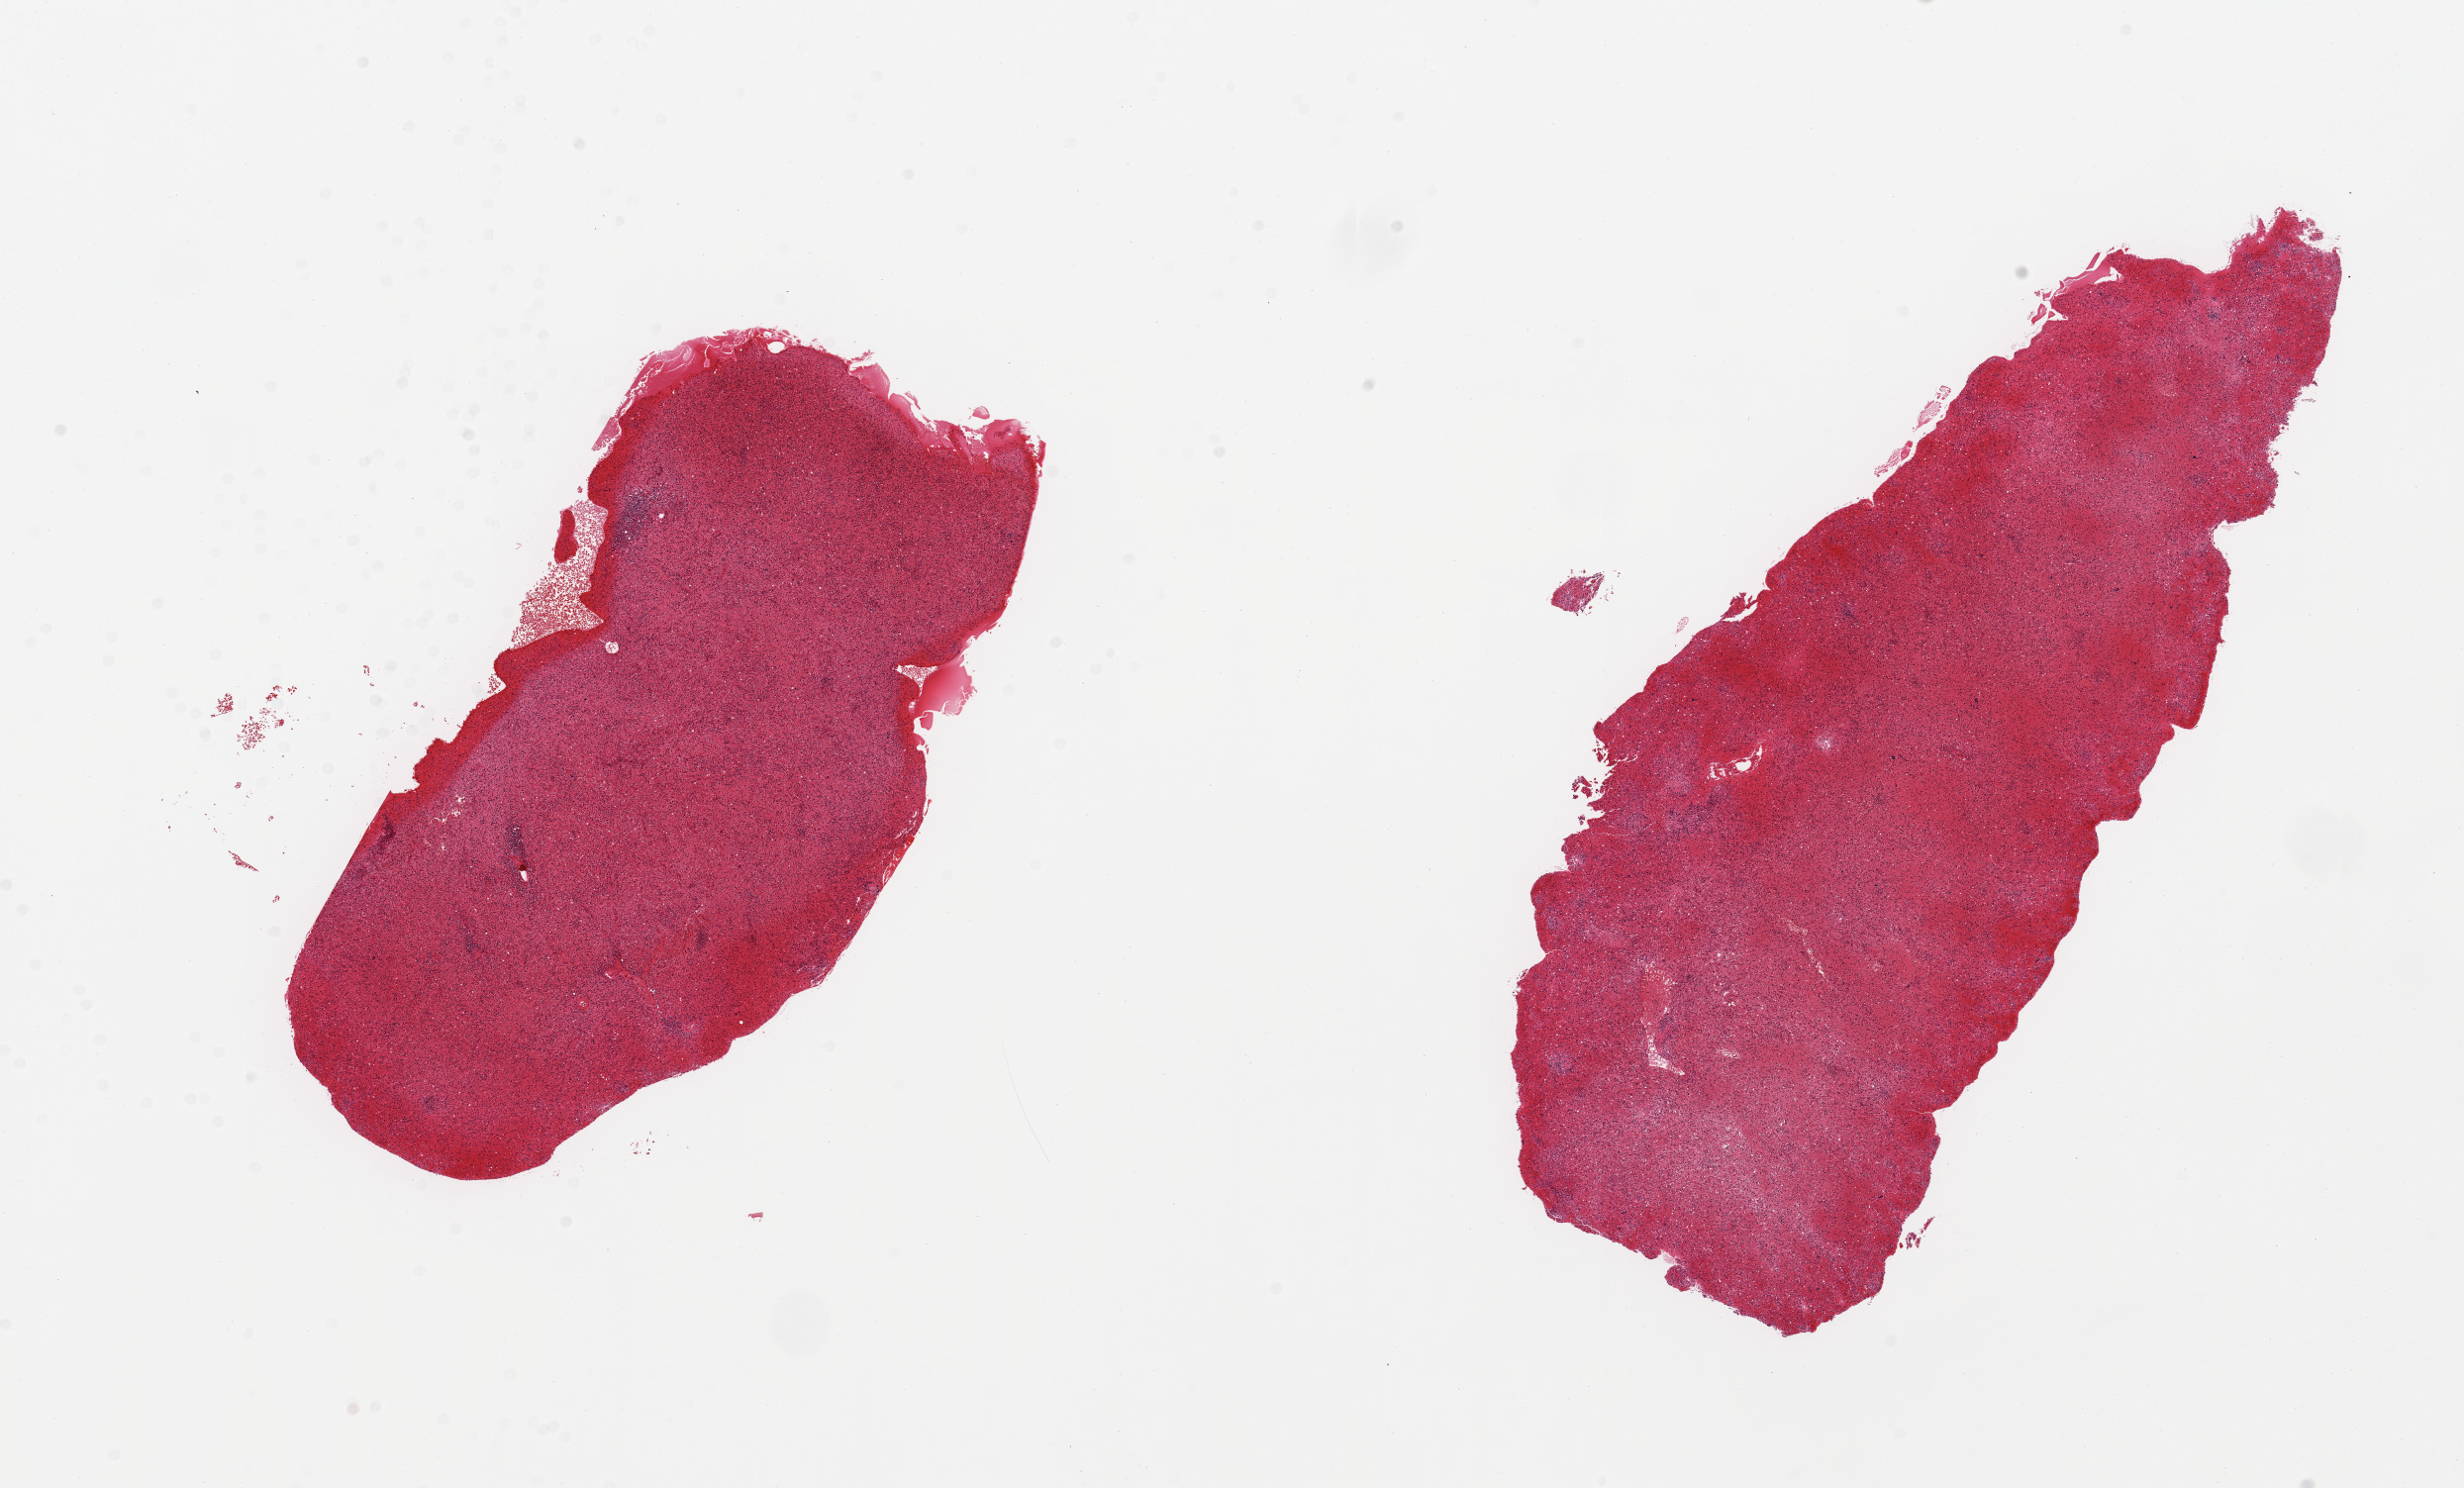
H&E whole-slide image, brightfield, shown as a low-resolution overview of the whole scanned area (about 19.7 x 11.9 mm), PAXgene-fixed paraffin-embedded (PFPE) section, sampled site (target tissue): spleen, tissue donor sample. Donor: male.
- pathologist's review note for this sample: 2 pieces; marked congestion